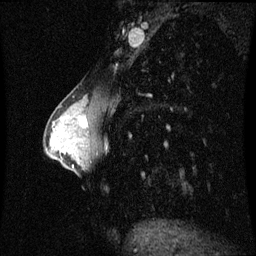
Breast MRI (dynamic contrast-enhanced), one sagittal slice. Position 27 of 60 along the scan axis. Dynamic contrast-enhanced series, image 2 of 3 at this slice position (ordered by acquisition). 1.5 T. TE 4.2 ms, TR 8.9 ms. 2 mm slice thickness. 256 × 256 image matrix, field of view 210 × 210 mm. Patient: female, 33 years. Case-level facts recorded for this patient, not image findings: setting: breast cancer imaged before/during neoadjuvant chemotherapy; receptor status: HER2-positive.
Annotated regions visible in this slice (semi-automatically segmented with operator editing):
- analysis volume of interest (the breast-tissue region the enhancement analysis was run in; not a lesion): bounding box <66,102,94,141> (left, top, right, bottom; pixels)
- tumour enhancement mask (voxels above the 70 % enhancement threshold inside the analysis volume of interest): <81,119,88,128>